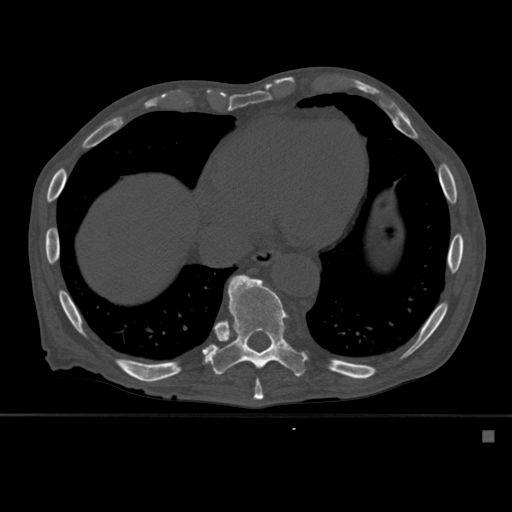
CT including the spine, one axial slice; position 318 of 527 along the scan axis; bone window (W 1800 / L 400 HU); 512 × 512 image matrix, field of view 373 × 373 mm. Male patient, age 78 years. Case-level facts recorded for this patient, not image findings: primary cancer: prostate.
Annotated regions visible in this slice (semi-automatically segmented with operator editing):
- T10 vertebra: bounding box [x1, y1, x2, y2] px = [204, 274, 306, 377]
- T9 vertebra: [253, 378, 264, 400]